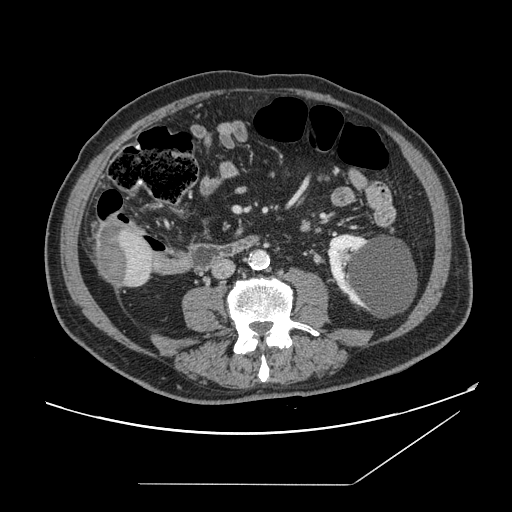
Contrast-enhanced abdominal CT, one axial slice. Position 29 of 166 along the scan axis. Intravenous contrast given. Soft-tissue window (W 400 / L 40 HU). 2.5 mm slice thickness. 512 × 512 image matrix. Male patient, age 80 years. Case-level facts recorded for this patient, not image findings: diagnosis: colorectal cancer liver metastases, imaged before liver resection; multiple liver metastases: no; largest metastasis: 2.2 cm.
Structures marked on this image (expert manual segmentation):
- liver: bounding box [x1, y1, x2, y2] px = [94, 224, 155, 288]
- liver metastasis: [98, 227, 129, 286]